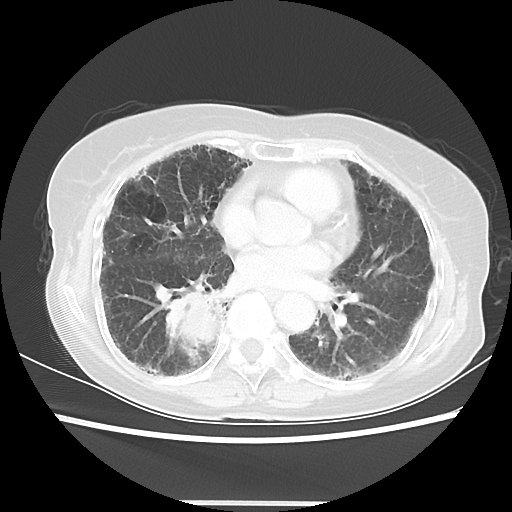
Chest CT, one axial slice; position 25 of 52 along the scan axis; reconstruction kernel LUNG; 120 kVp; lung window (W 1500 / L -600 HU); 5 mm slice thickness; 512 × 512 image matrix, field of view 325 × 325 mm. Patient: female, 71 years. From the clinical record (not read from this slice): clinical TNM (as recorded): T3 N0 M0.
Outlined on this slice (bounding box drawn by a radiologist):
- lung tumour (recorded histology: squamous cell carcinoma): box from (x=162, y=286) to (x=231, y=359) px